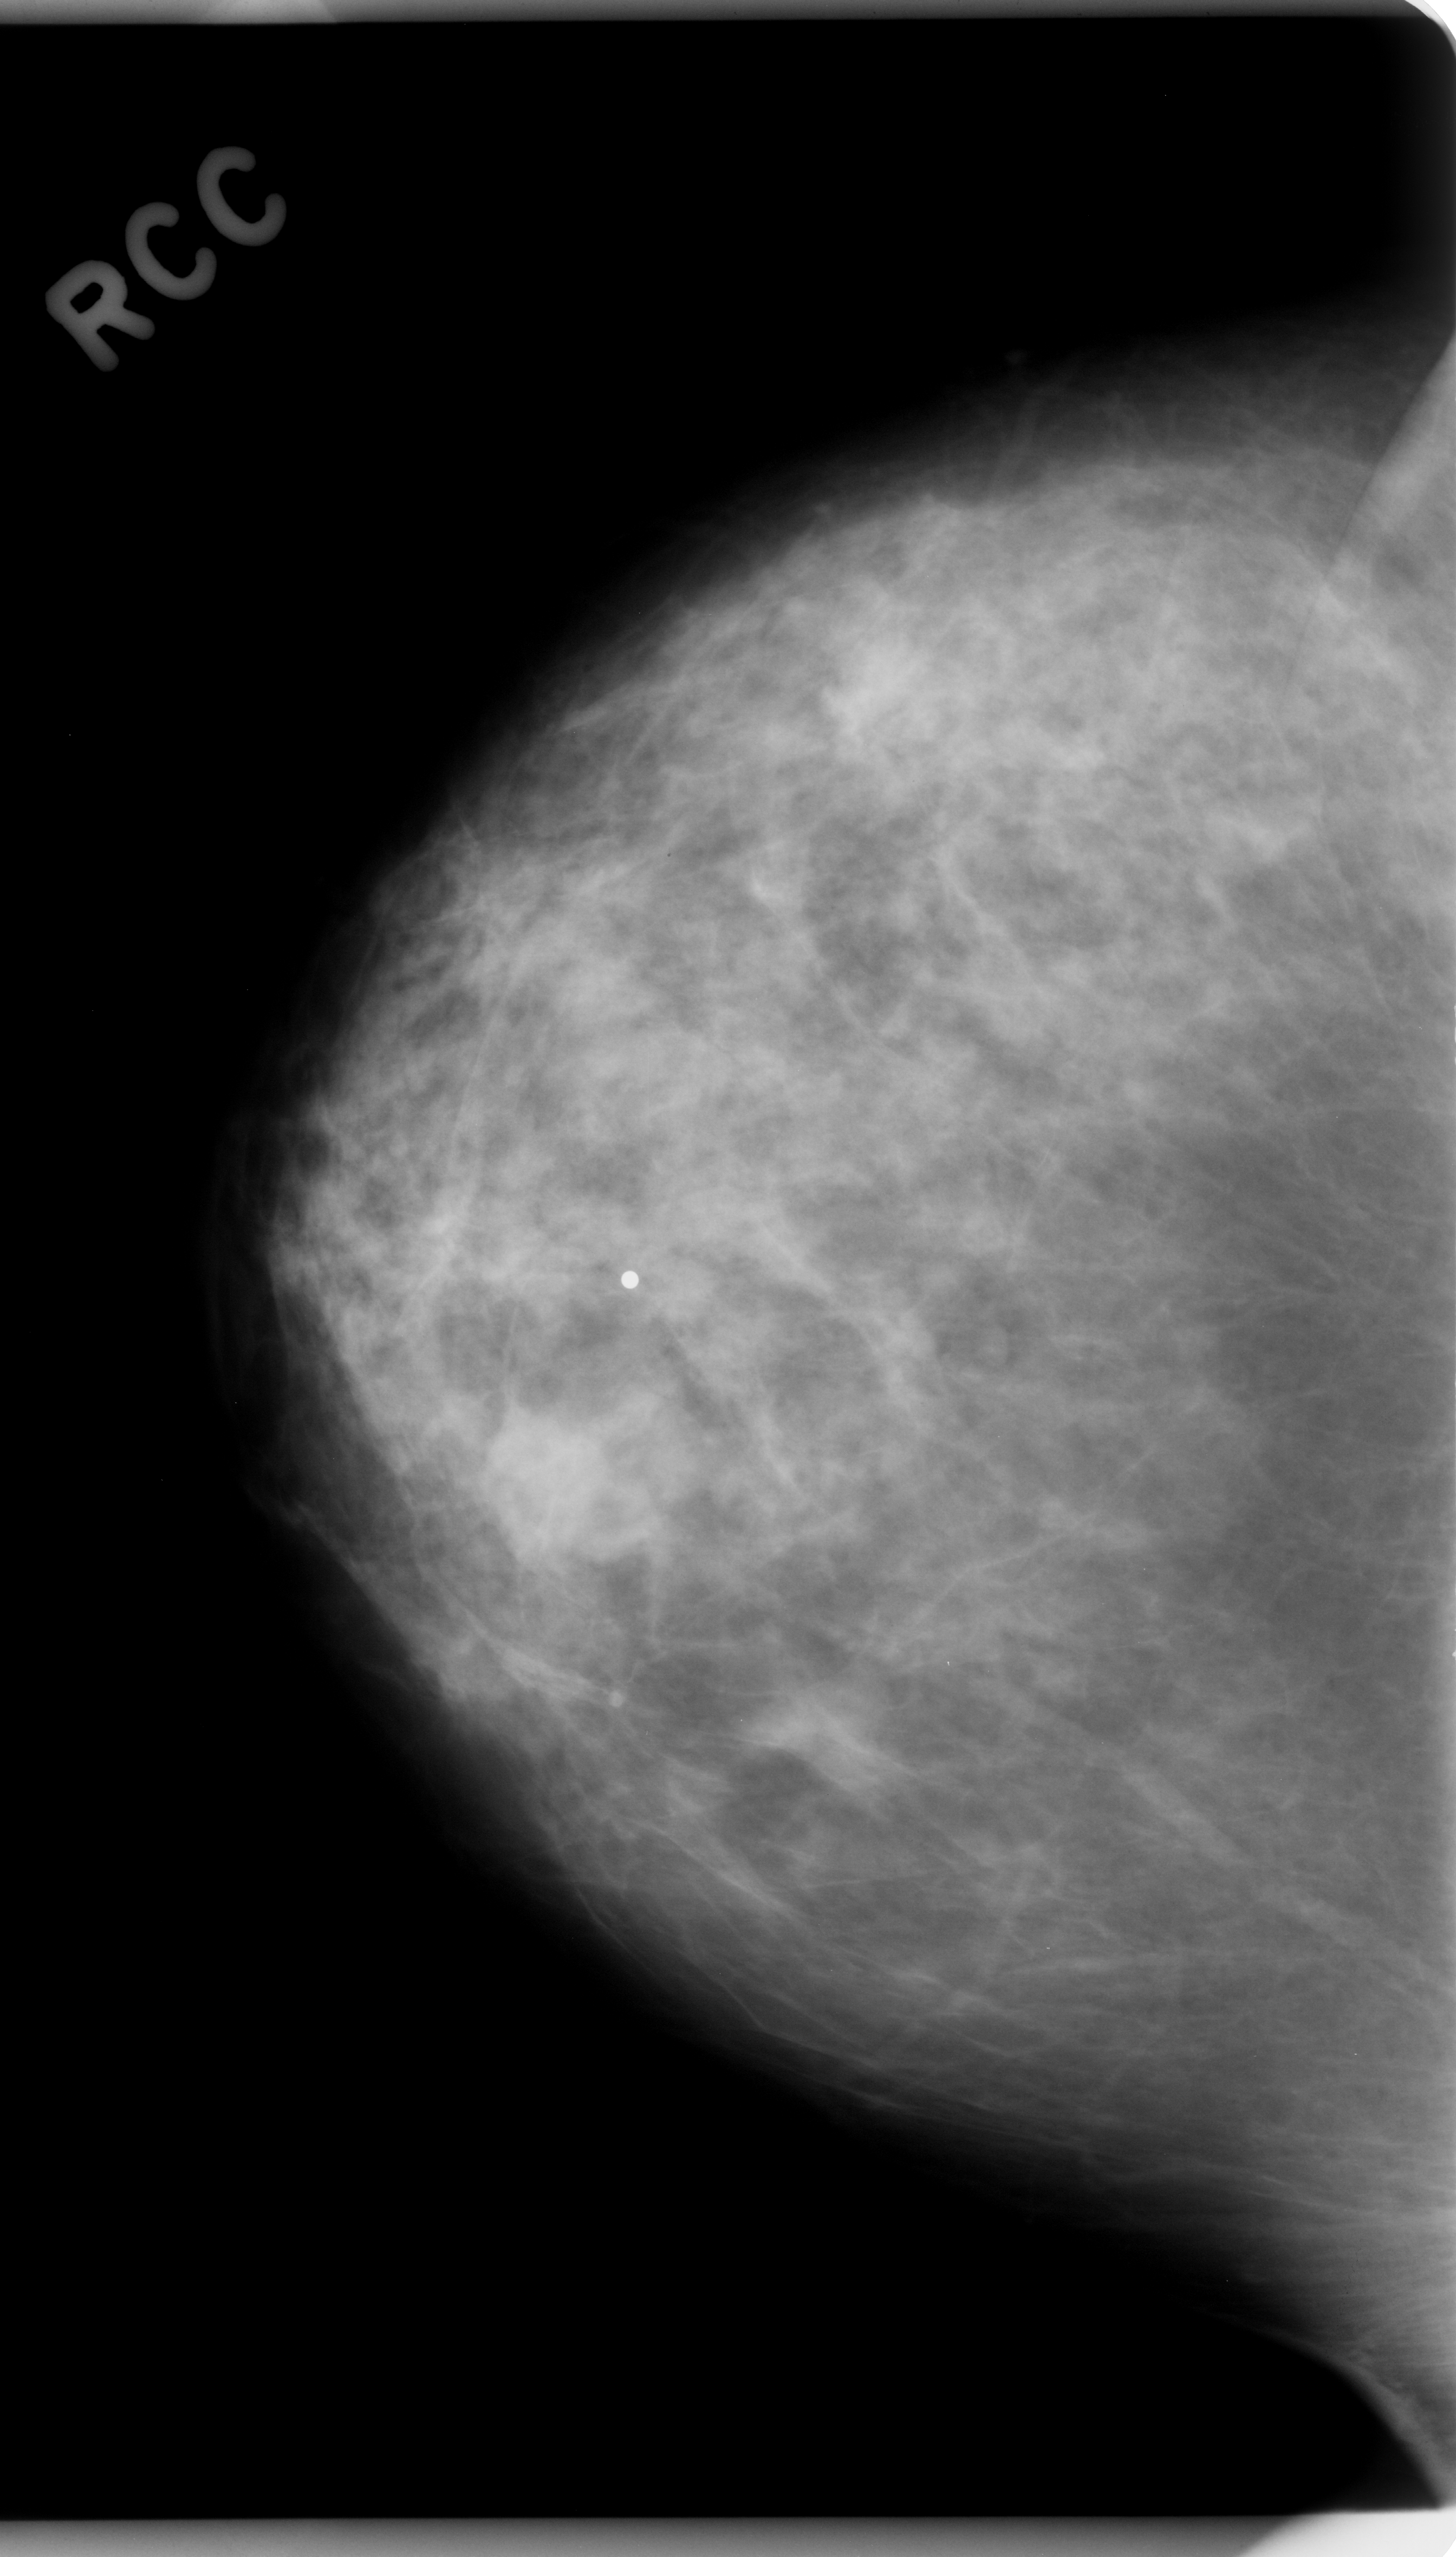
Scanned film-screen mammogram; right breast; CC view; breast composition: scattered fibroglandular densities (BI-RADS density category 2 of 4); 1456 × 2557 image matrix.
Marked abnormalities (boxes around the expert regions of interest):
- mass, shape oval, margins ill defined; BI-RADS assessment category 4; subtlety rating 4 on a 1 (subtle) to 5 (obvious) scale; pathology (as recorded): benign: bounding box (x1, y1, x2, y2) in pixels: (414, 1350, 680, 1616)